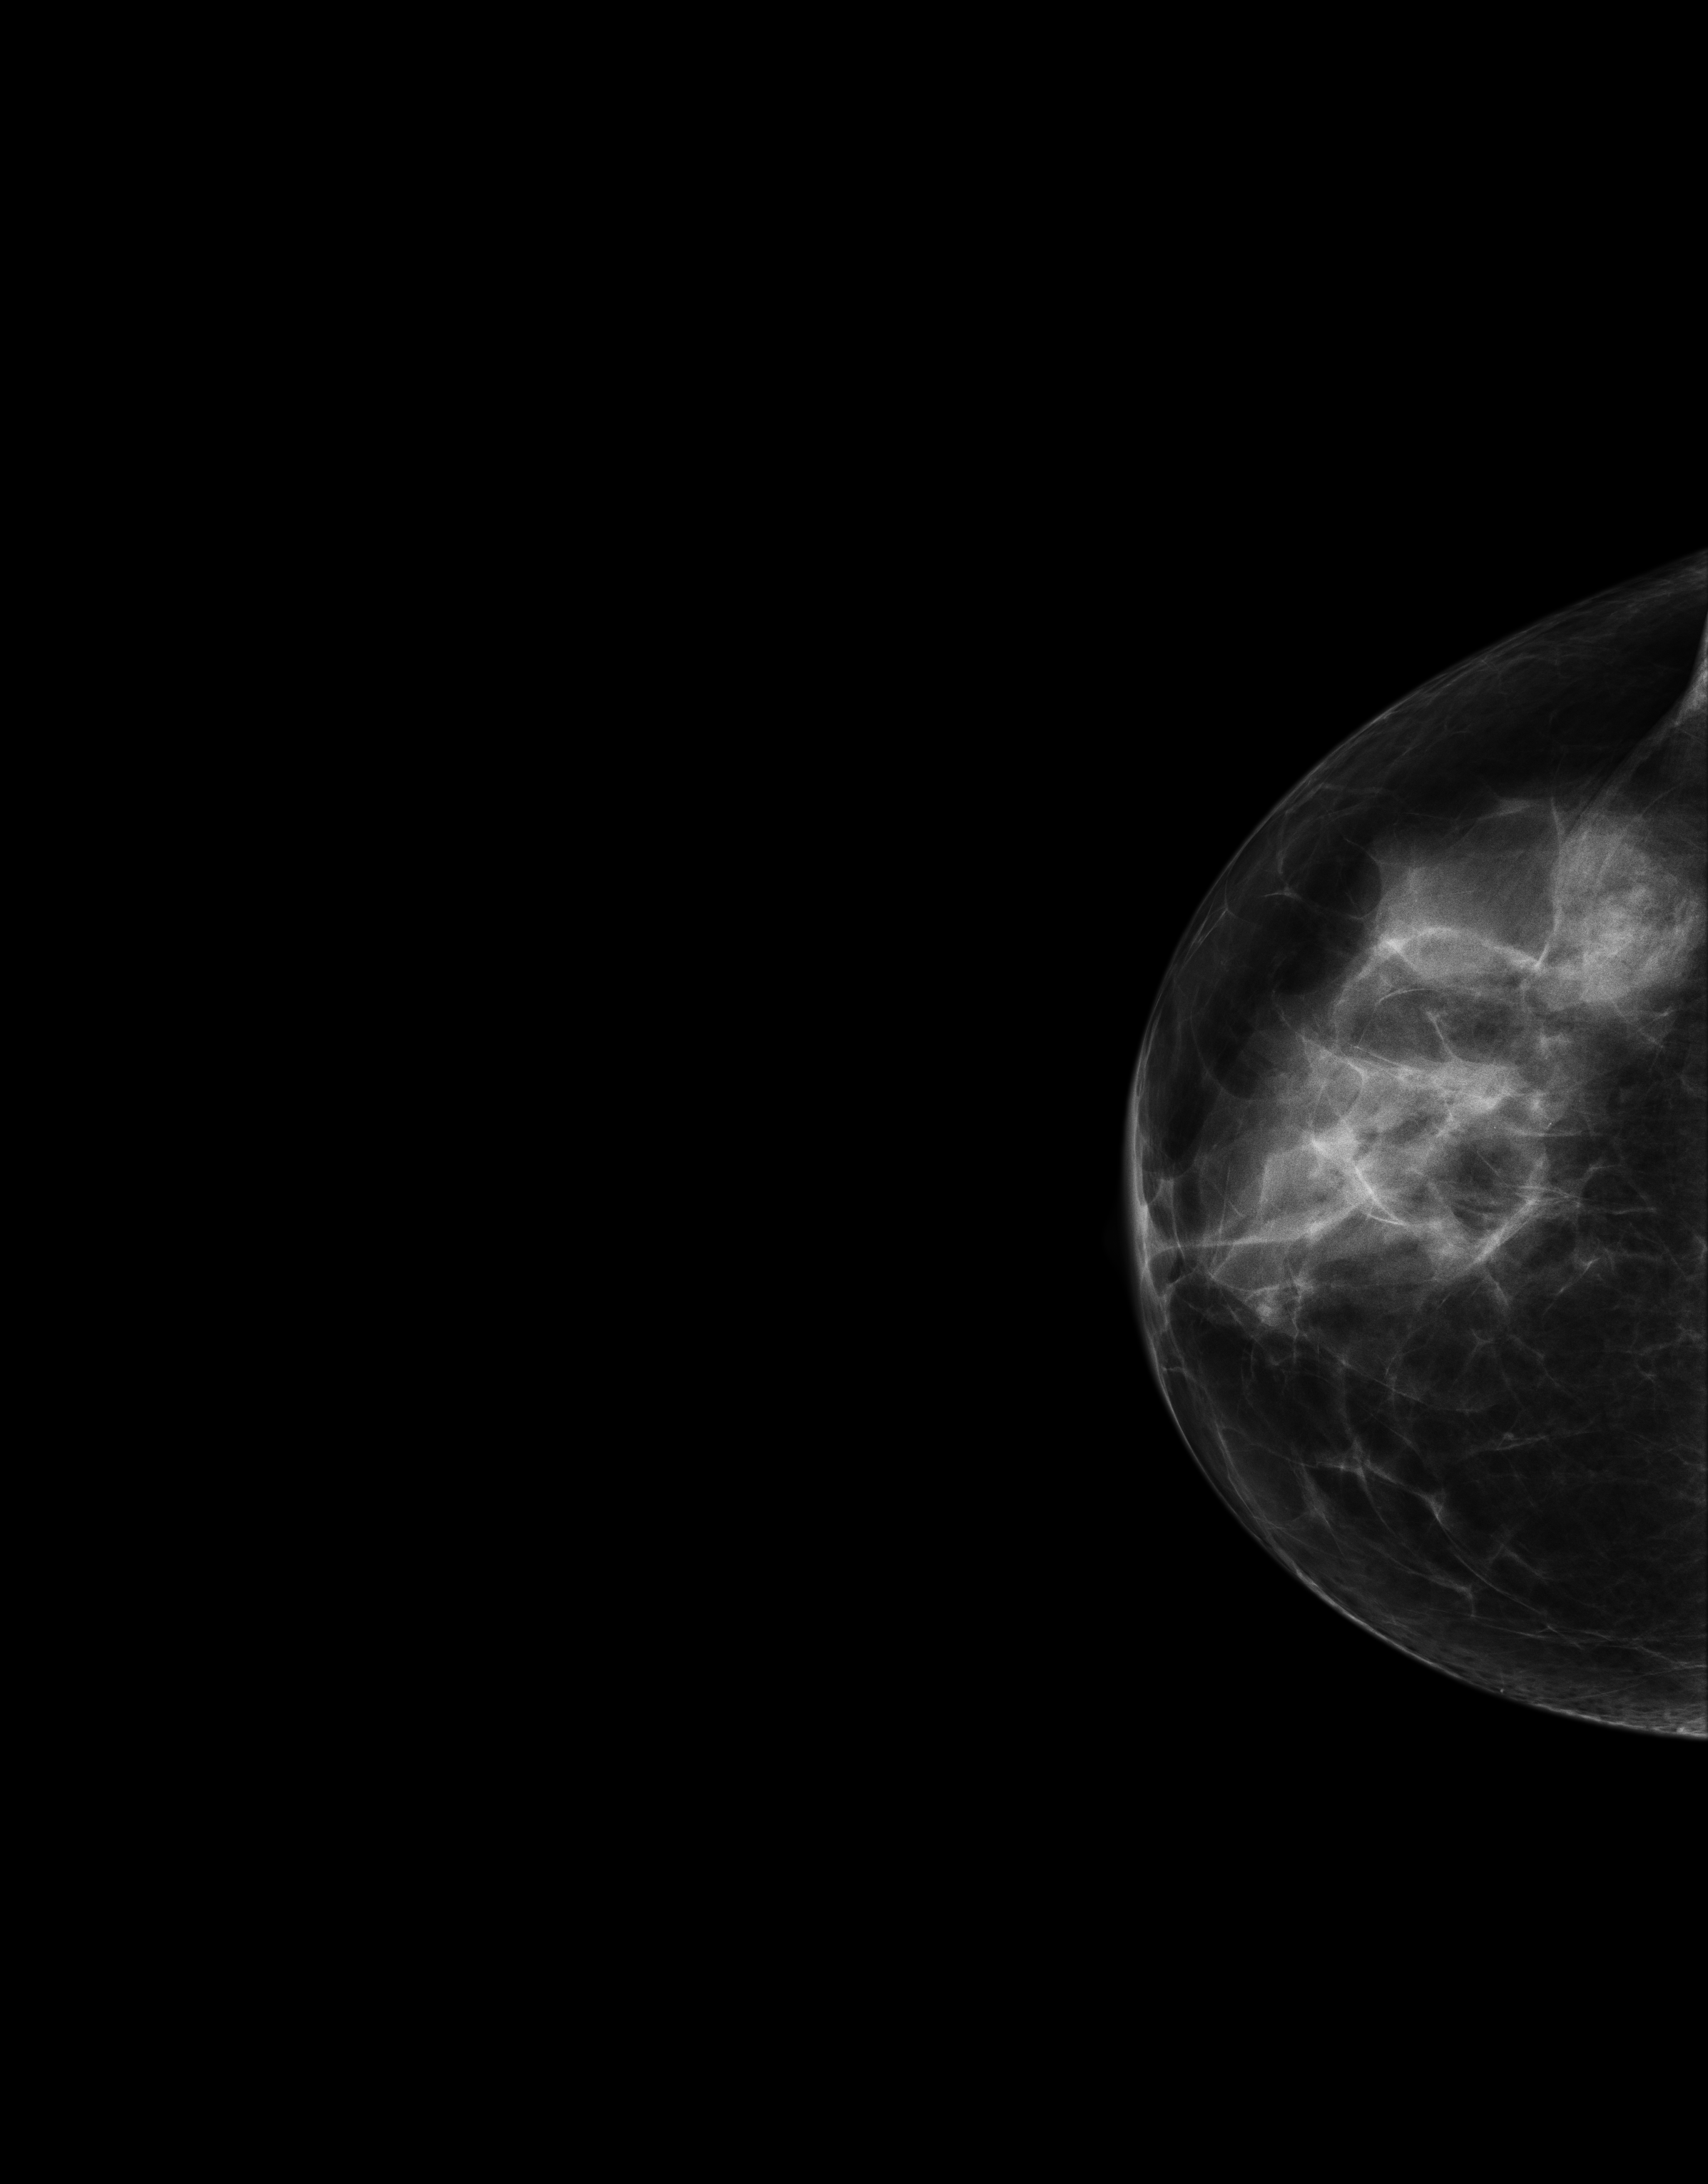
Annual screening mammography examination; compressed breast thickness 55 mm. Patient aged 52 years (female).
Image type: full-field digital mammogram. Breast: right. Projection: CC view.